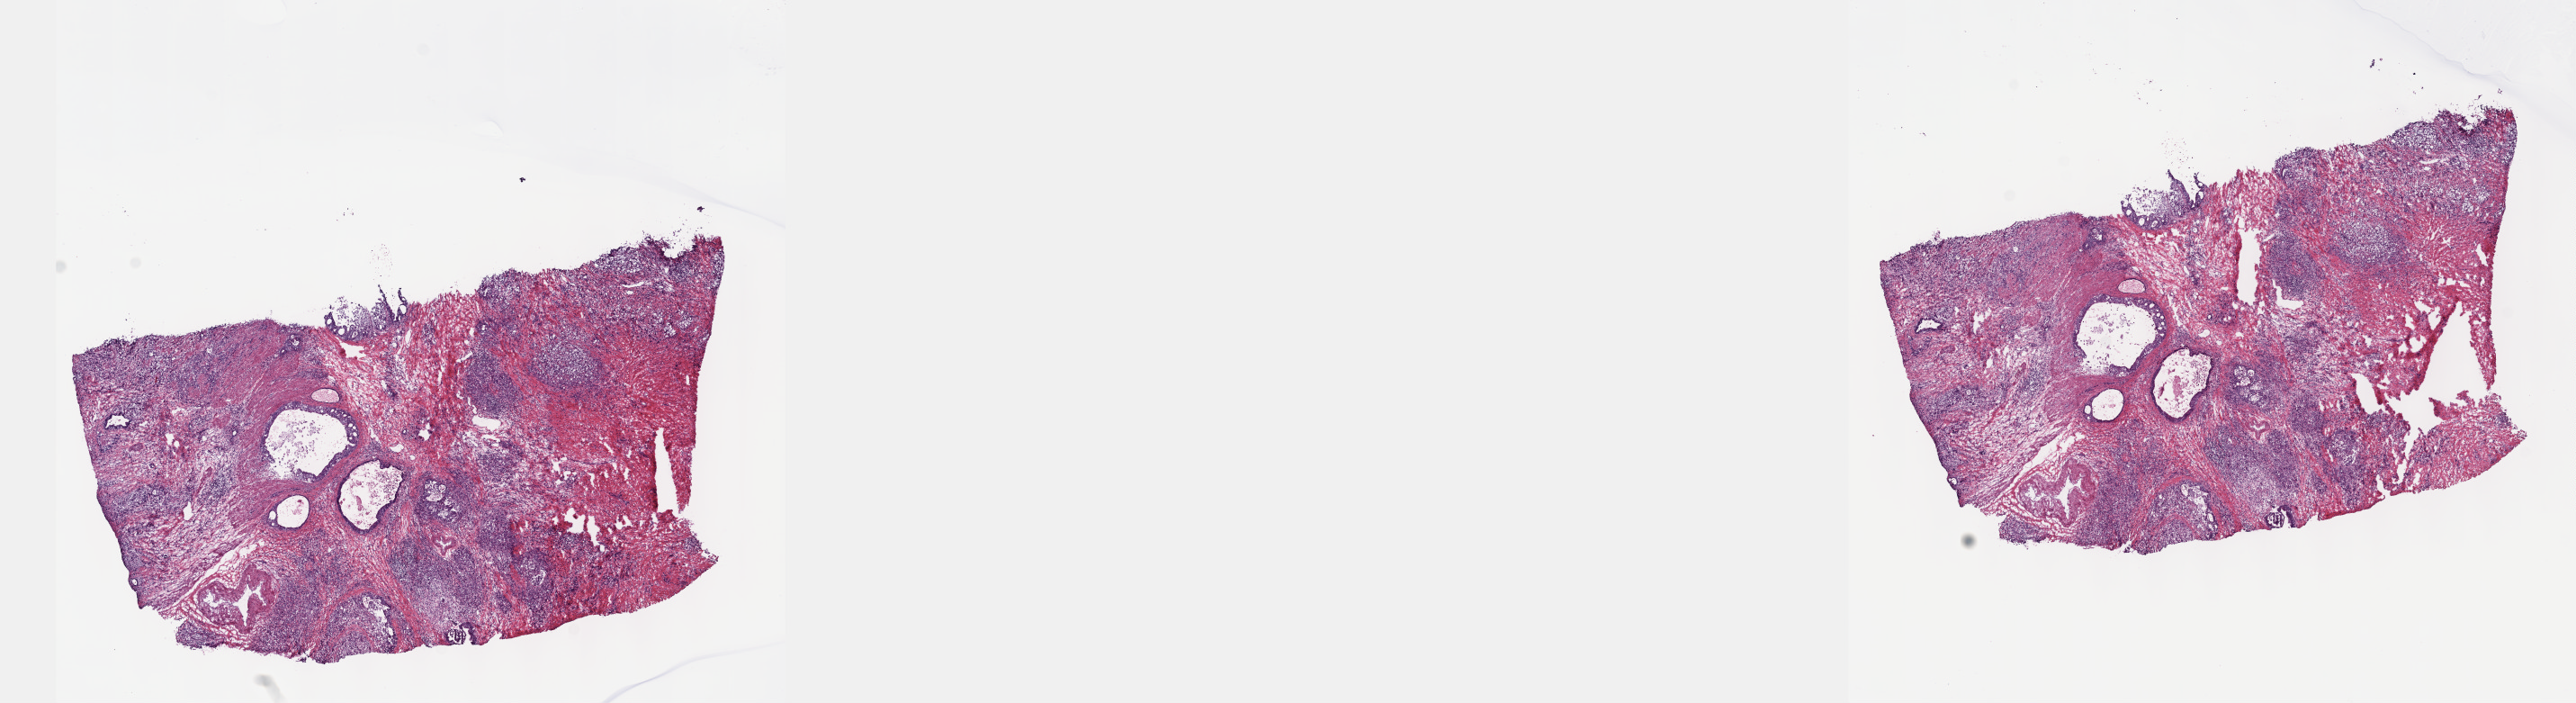
Digitized Hematoxylin and eosin (H&E) stained tissue section (whole slide), low-resolution overview of the scanned area, about 23.1 x 6.3 mm; frozen section; sample: primary tumour, stomach. Female, age 50 years at initial diagnosis. Composition of this section per pathologist review: tumour cells 70%, tumour nuclei 70%.
Histologic diagnosis: Tubular adenocarcinoma (cardia, NOS).